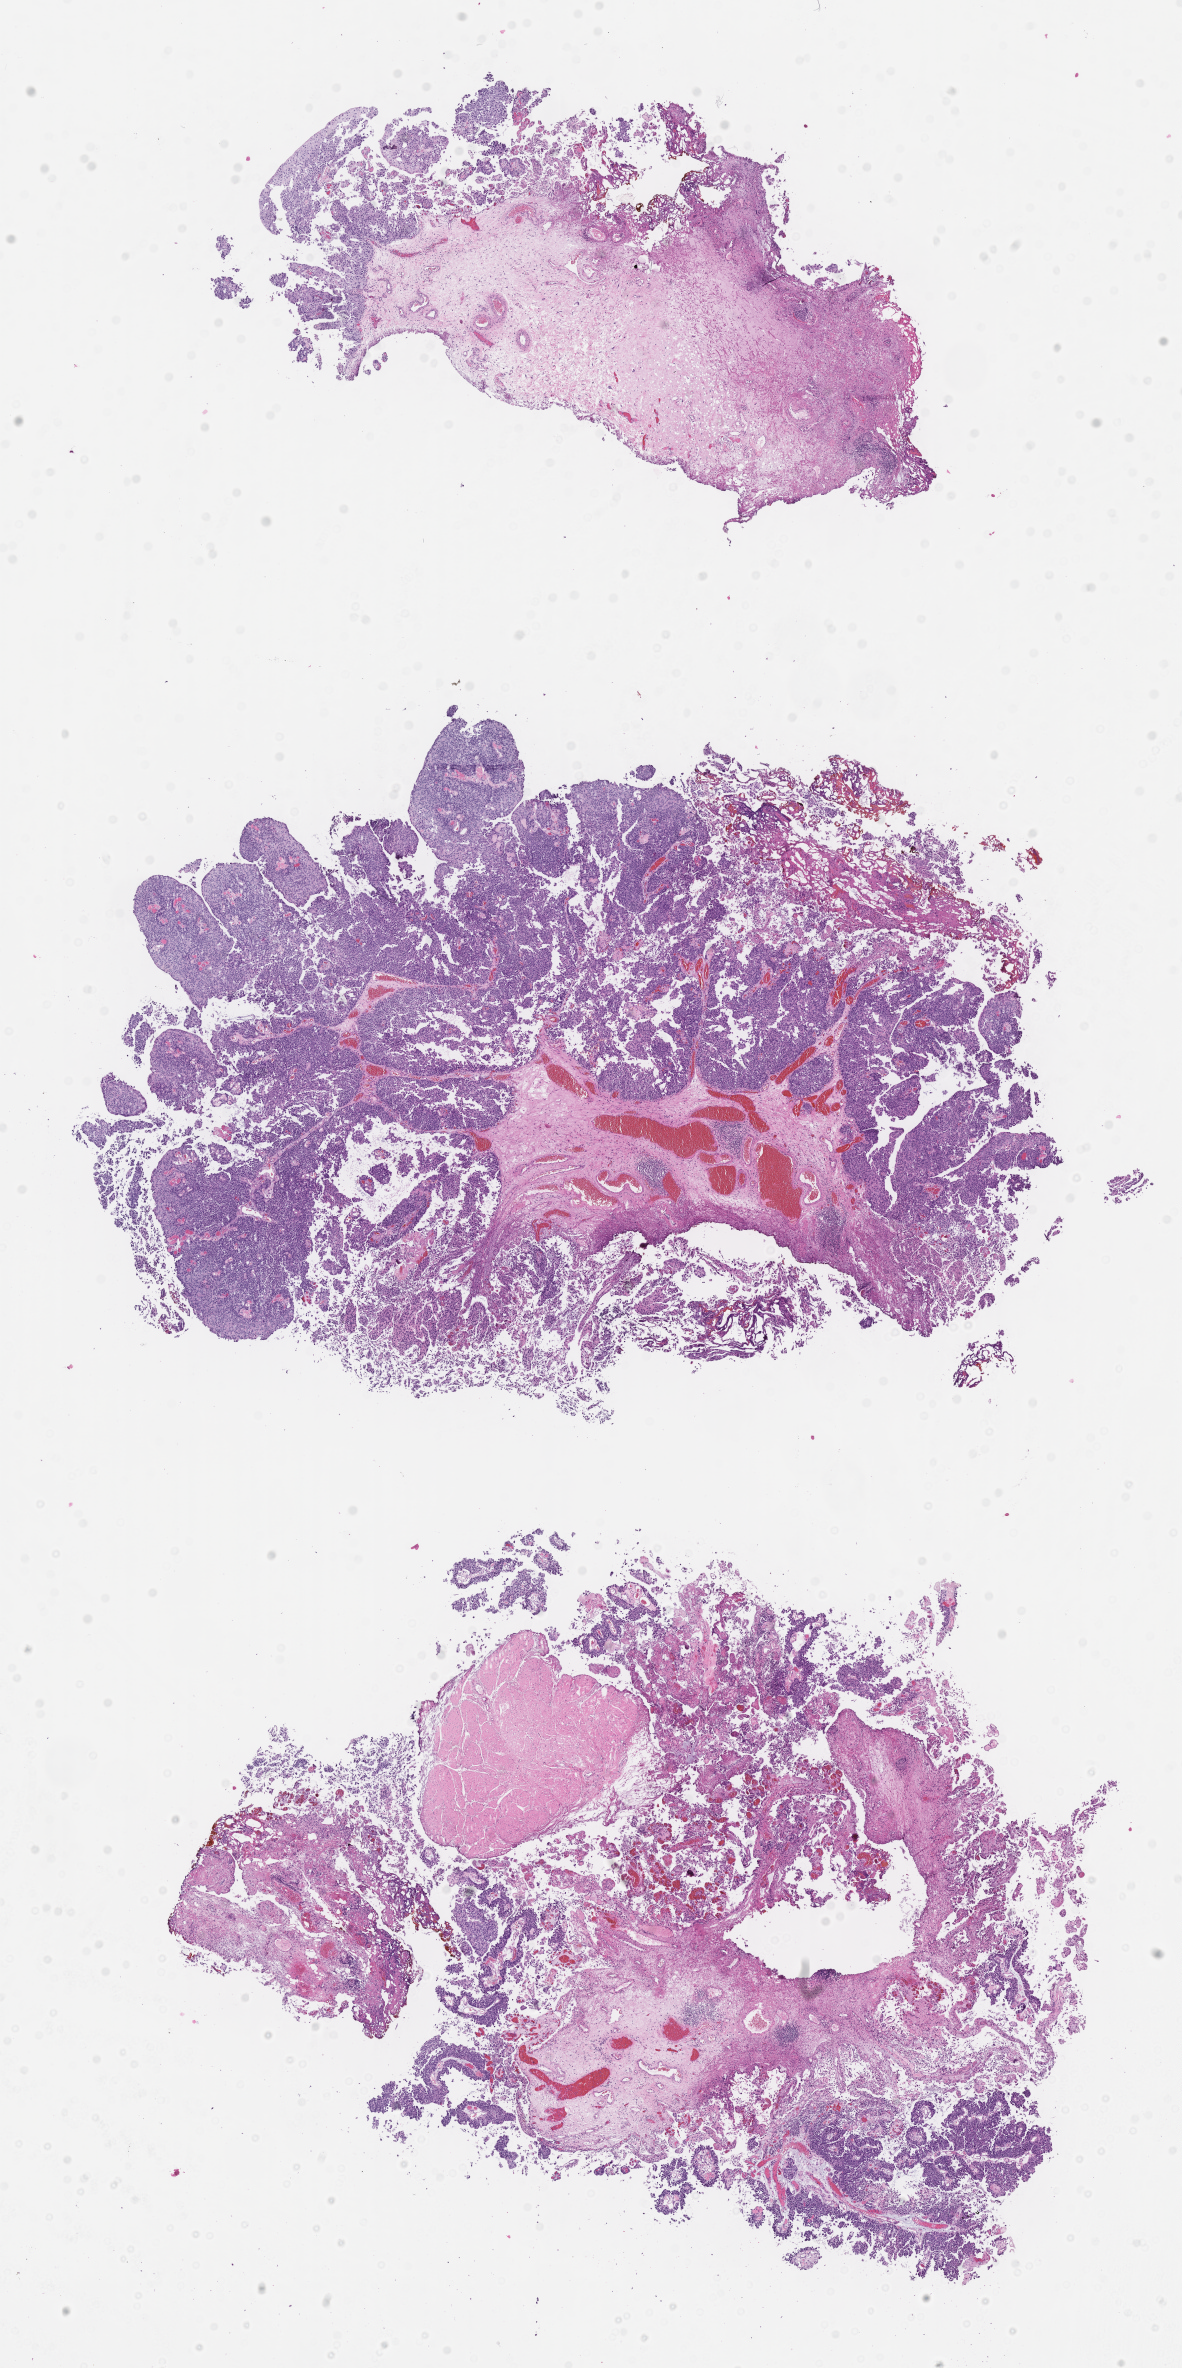
Whole-slide image, hematoxylin and eosin (H&E) stain — shown as a low-resolution overview of the whole scanned area (about 9.5 x 19.1 mm), FFPE section, specimen: primary tumor, anatomic site: bladder. Male patient; age at initial diagnosis 62 years. Composition of this section per pathologist review: tumor cells 70%, tumor nuclei 90%, stromal cells 30%, necrosis 0%, normal cells 0%. Inflammatory infiltration, as recorded: lymphocyte infiltration 0%, monocyte infiltration 0%, neutrophil infiltration 0%.
* histologic diagnosis: Papillary urothelial carcinoma, non-invasive
* section: bottom of the tissue portion